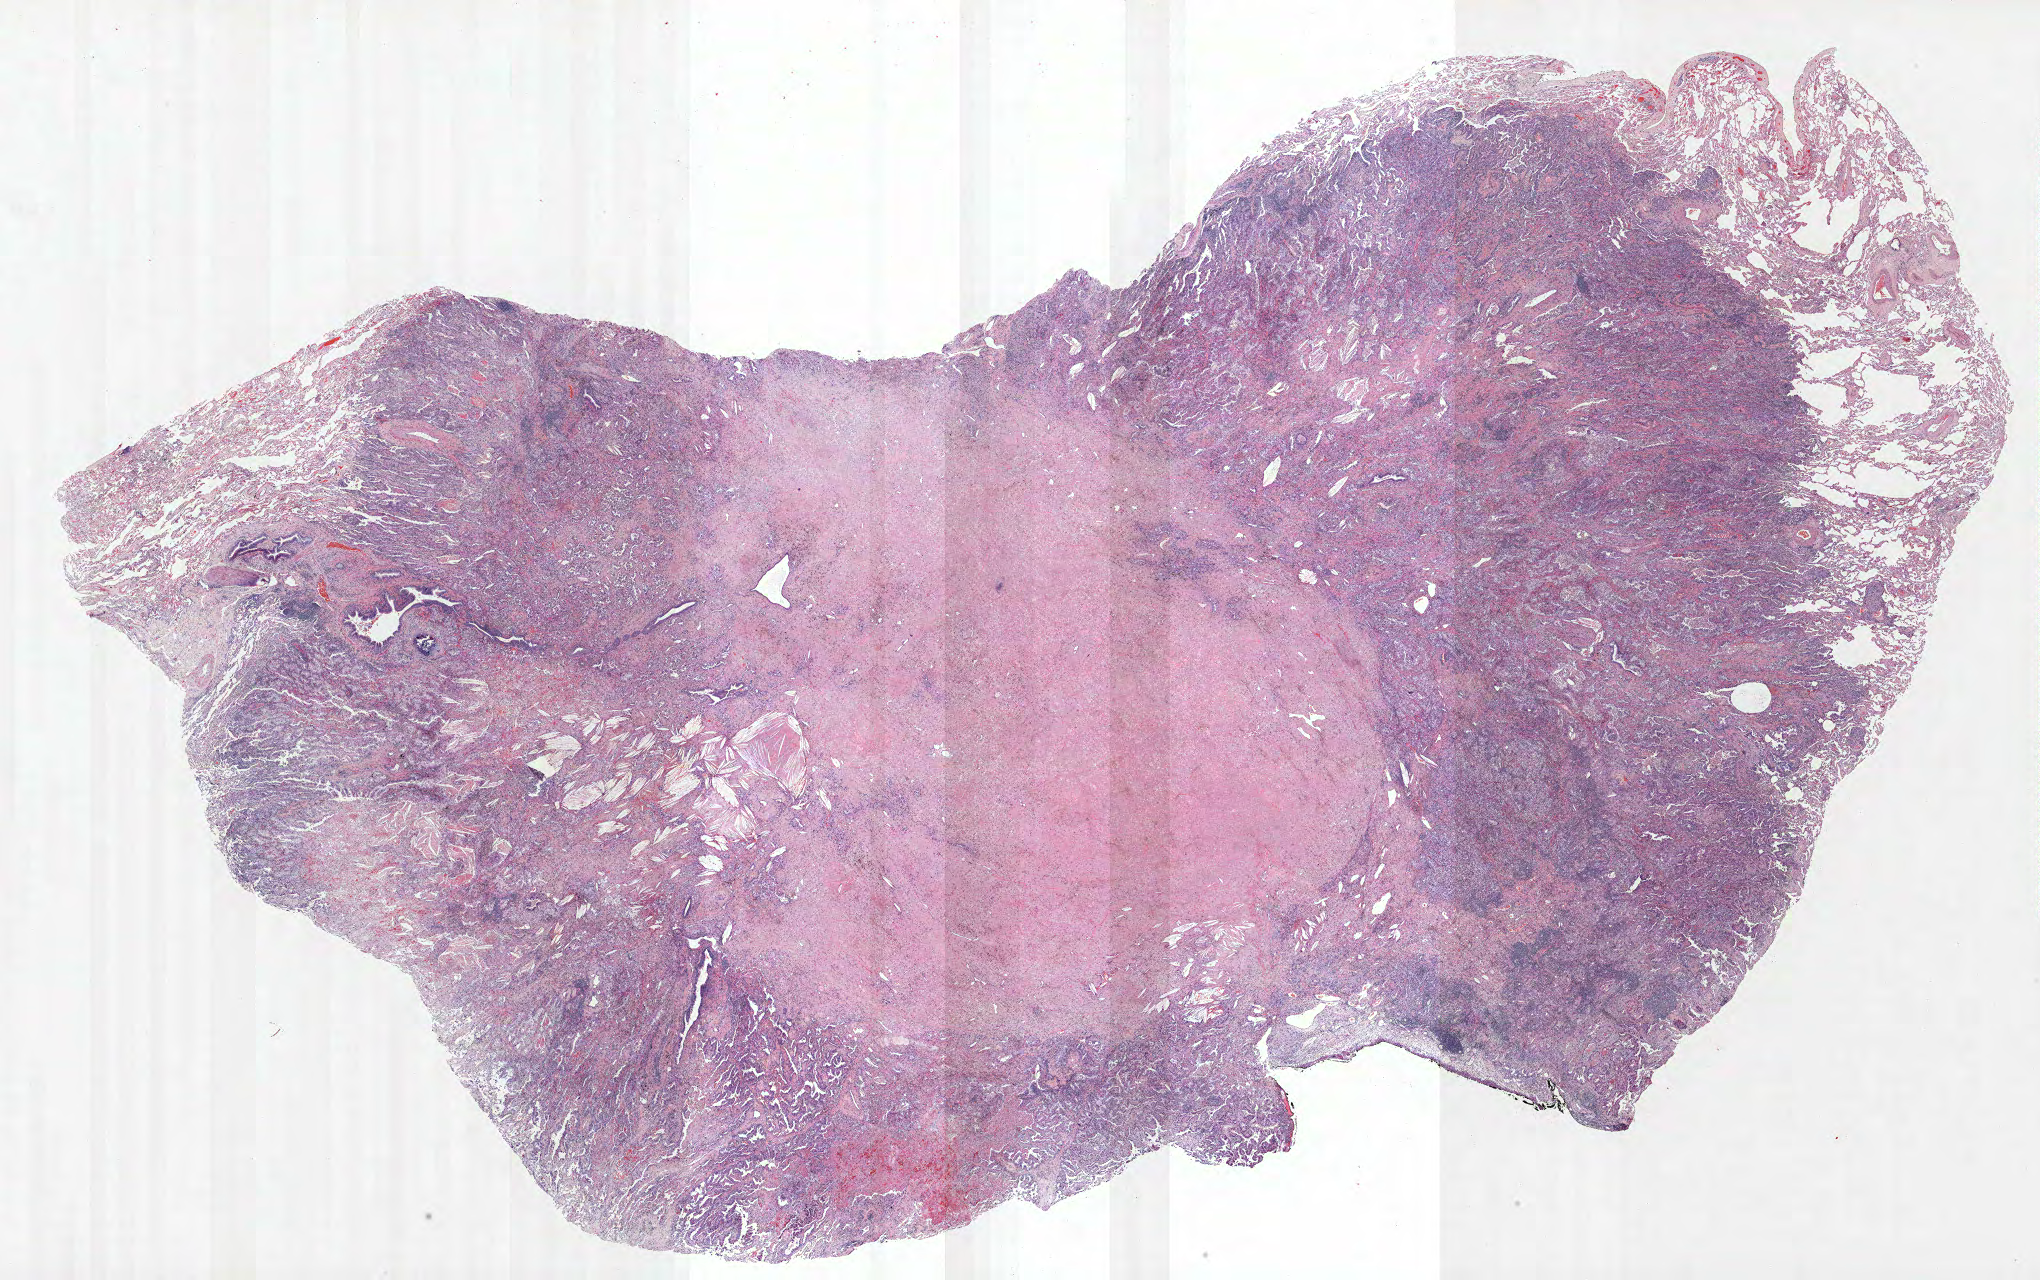
Whole-slide histology image, H&E, shown as a low-resolution overview of the whole scanned area (about 32.6 x 20.5 mm); formalin-fixed paraffin-embedded (FFPE) section; lung tissue. Male patient, aged 64 at enrolment. Current smoker at enrolment. Grade: moderately differentiated (G2).
Primary tumour location (clinical record): right lower lobe. Tumour size (pathology): 28 mm. ICD-O-3 topography: lower lobe of lung (C34.3). Participant's lung-cancer diagnosis: Adenocarcinoma, NOS (ICD-O-3 8140/3). Stage (AJCC 6th edition): IA.